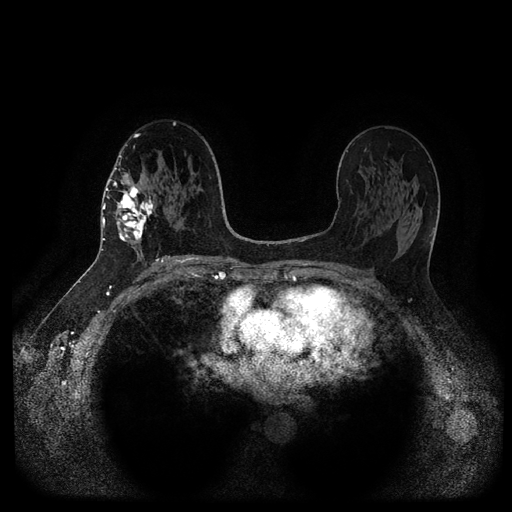
Breast MRI (dynamic contrast-enhanced, multi-phase), one axial slice. Slice 58 of 116 in the series (ordered by position). Dynamic contrast-enhanced series, time point 2 of 5 at this slice position (early post-contrast). 1.5 T. TE 2.6 ms, TR 5.3 ms. 2 mm slice thickness. 512 × 512 image matrix. Patient: female, 58 years.
Structures marked on this image (semi-automatically segmented with operator editing):
- breast lesion (labelled 'tumour' in the annotation; benign lesions carry a separate 'benign' label): box from (x=114, y=181) to (x=157, y=248) px